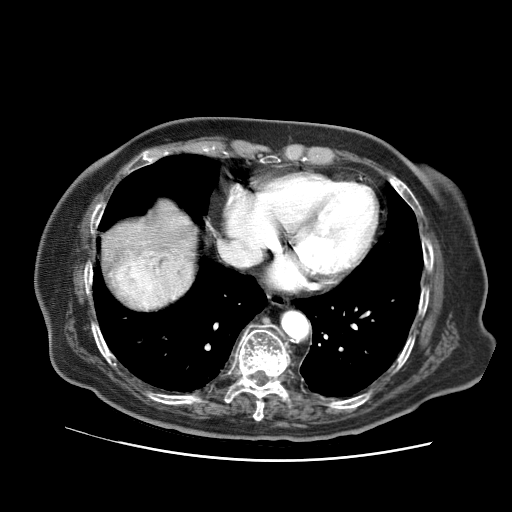
Contrast-enhanced abdominal CT (liver protocol), one axial slice; position 63 of 73 along the scan axis; reconstruction kernel STANDARD; 120 kVp; soft-tissue window (W 400 / L 40 HU); 2.5 mm slice thickness; 512 × 512 image matrix. Case-level facts recorded for this patient, not image findings: diagnosis: hepatocellular carcinoma (patient treated with transarterial chemoembolisation; whether this scan precedes or follows treatment is not stated here); TNM stage (as recorded): Stage-I; Child-Pugh class: A; tumour differentiation: well differentiated; tumour nodularity: uninodular.
Outlined on this slice (semi-automatic segmentation, software-assisted and operator-edited):
- abdominal aorta: bounding box [x1, y1, x2, y2] px = [282, 312, 309, 340]
- liver parenchyma outside the tumour (the mass and vessels are separate outlines, so this box may not span the whole liver): [100, 198, 198, 311]
- mass: [112, 253, 191, 308]